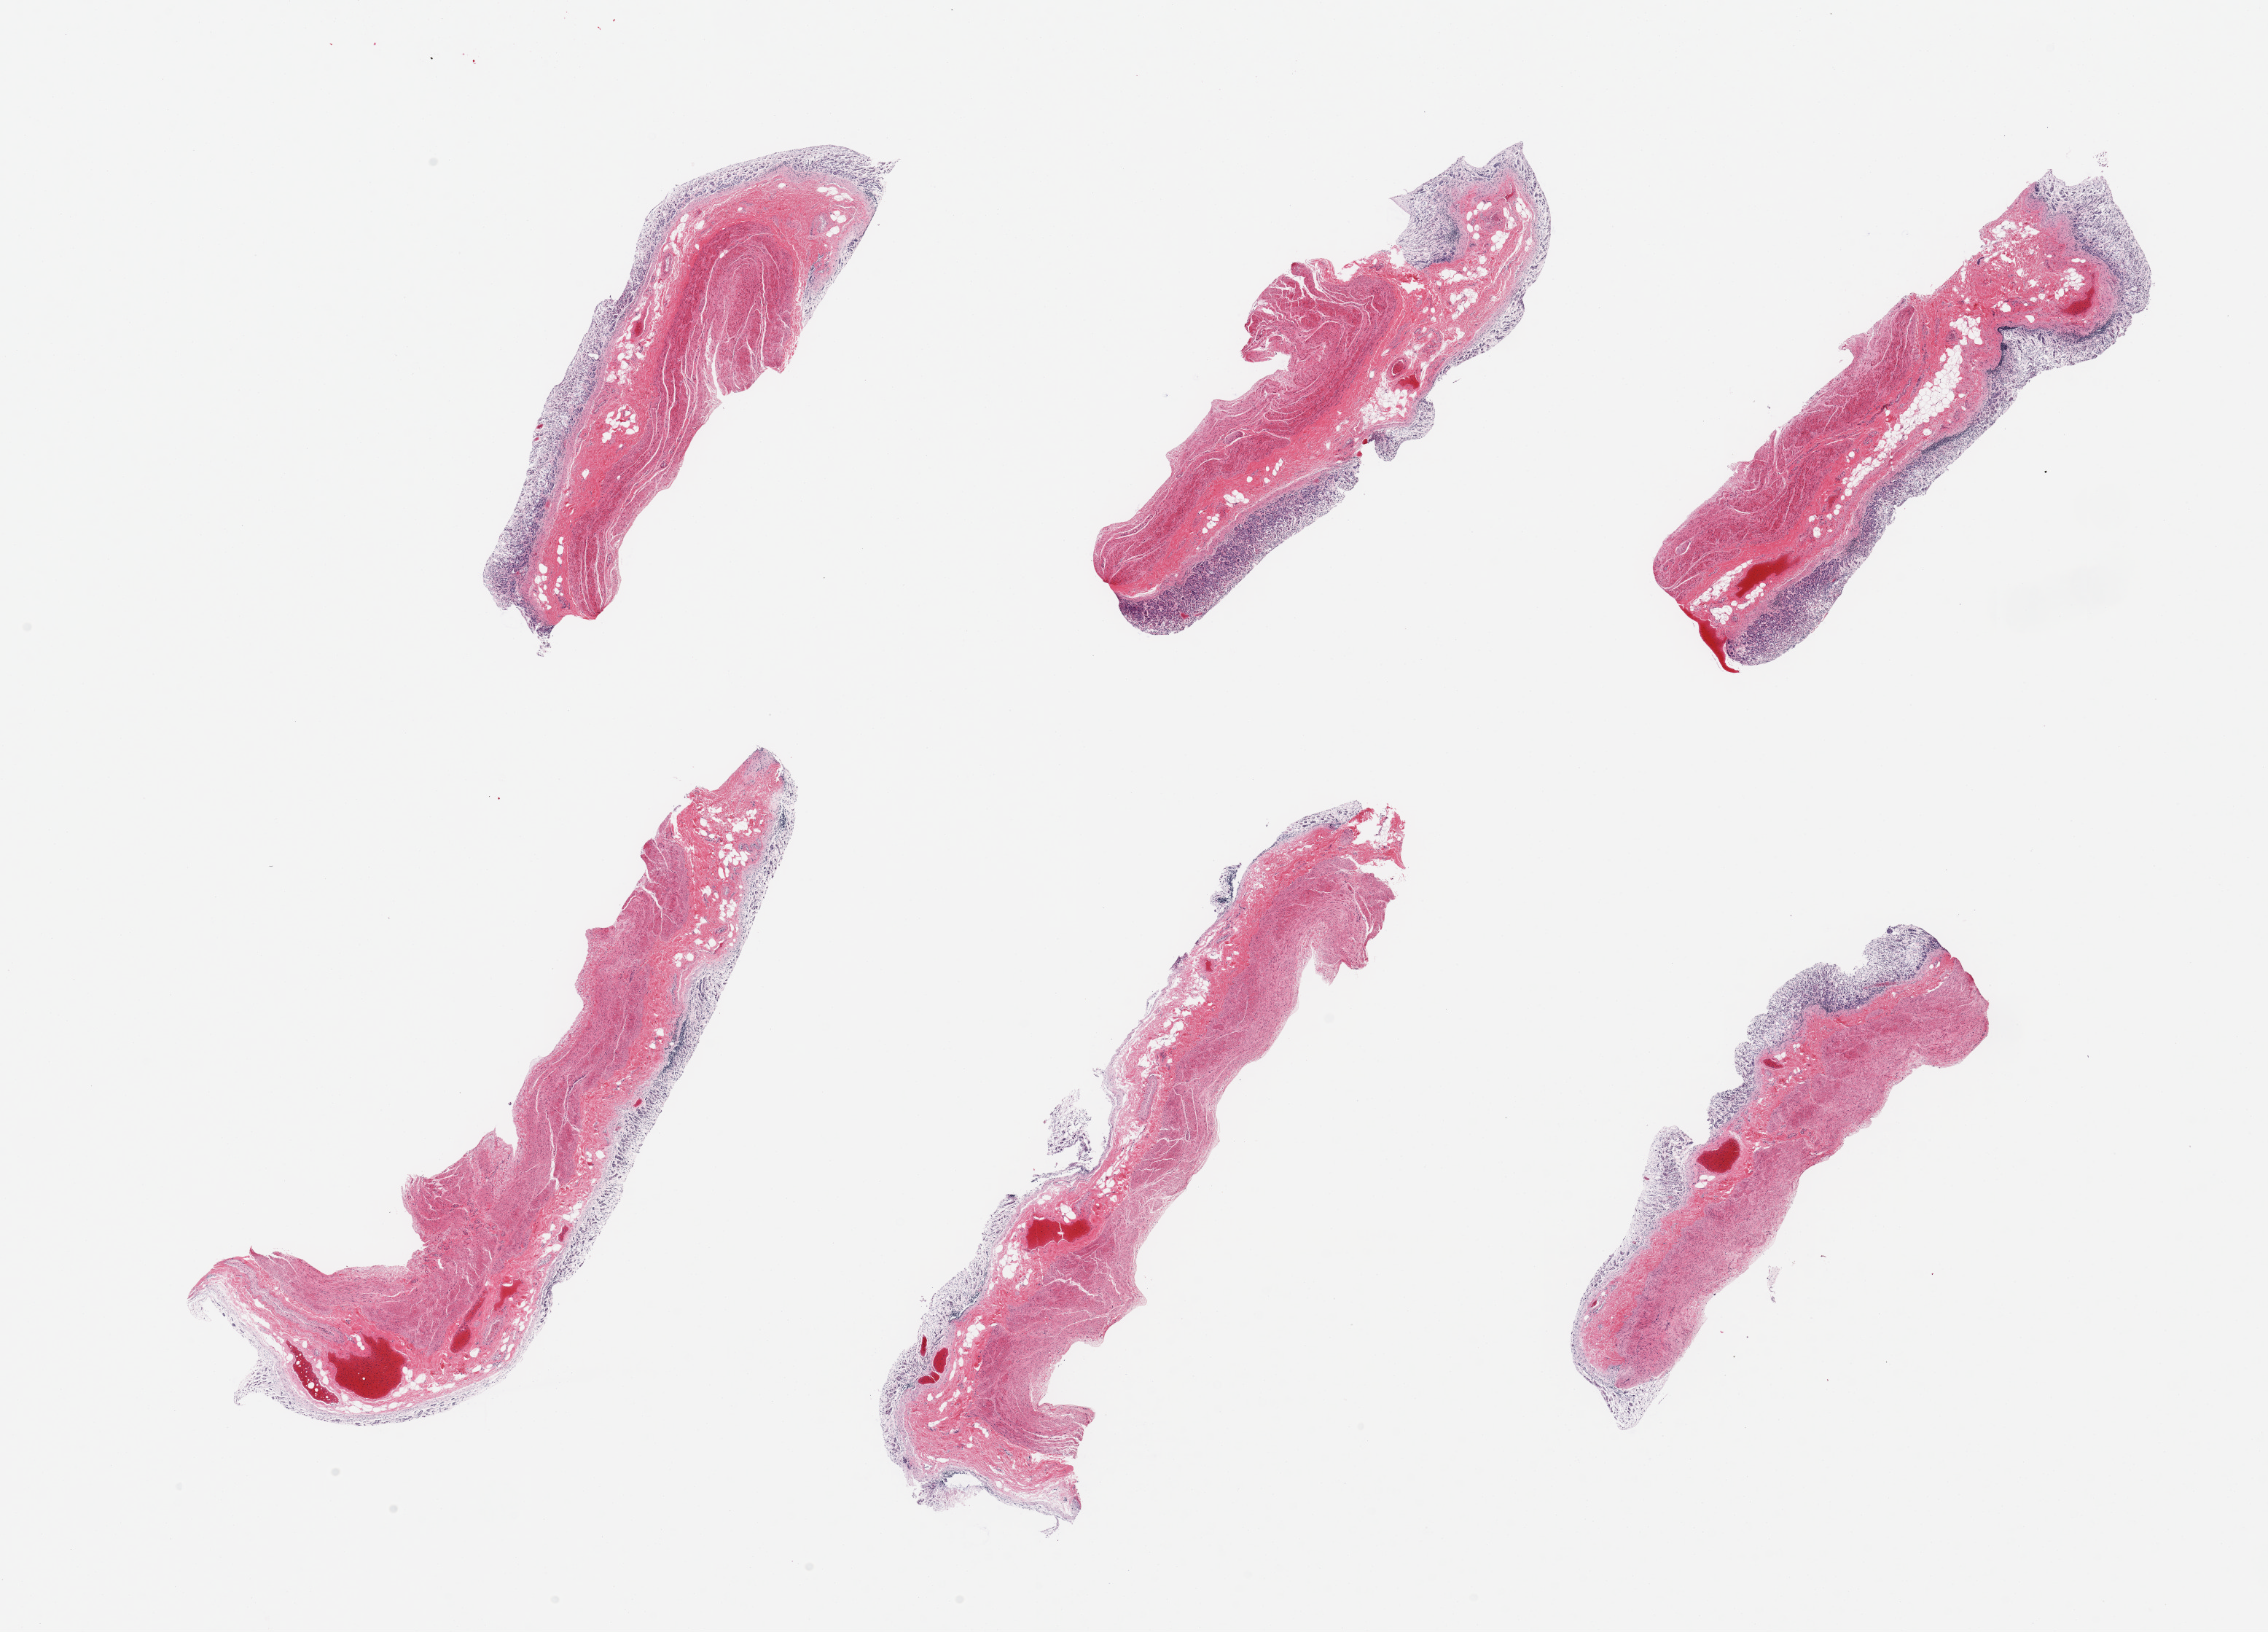
Digitized haematoxylin and eosin-stained section, brightfield, a low-resolution overview of the entire scanned area, about 24.6 x 17.7 mm, PAXgene-fixed paraffin-embedded (PFPE) section, sampled site (target tissue): stomach, tissue donor sample. Female donor.
Reviewer comment on this tissue sample: 6 pieces, mucosa up to ~0.5mm but advanced autolysis, partially sloughing.